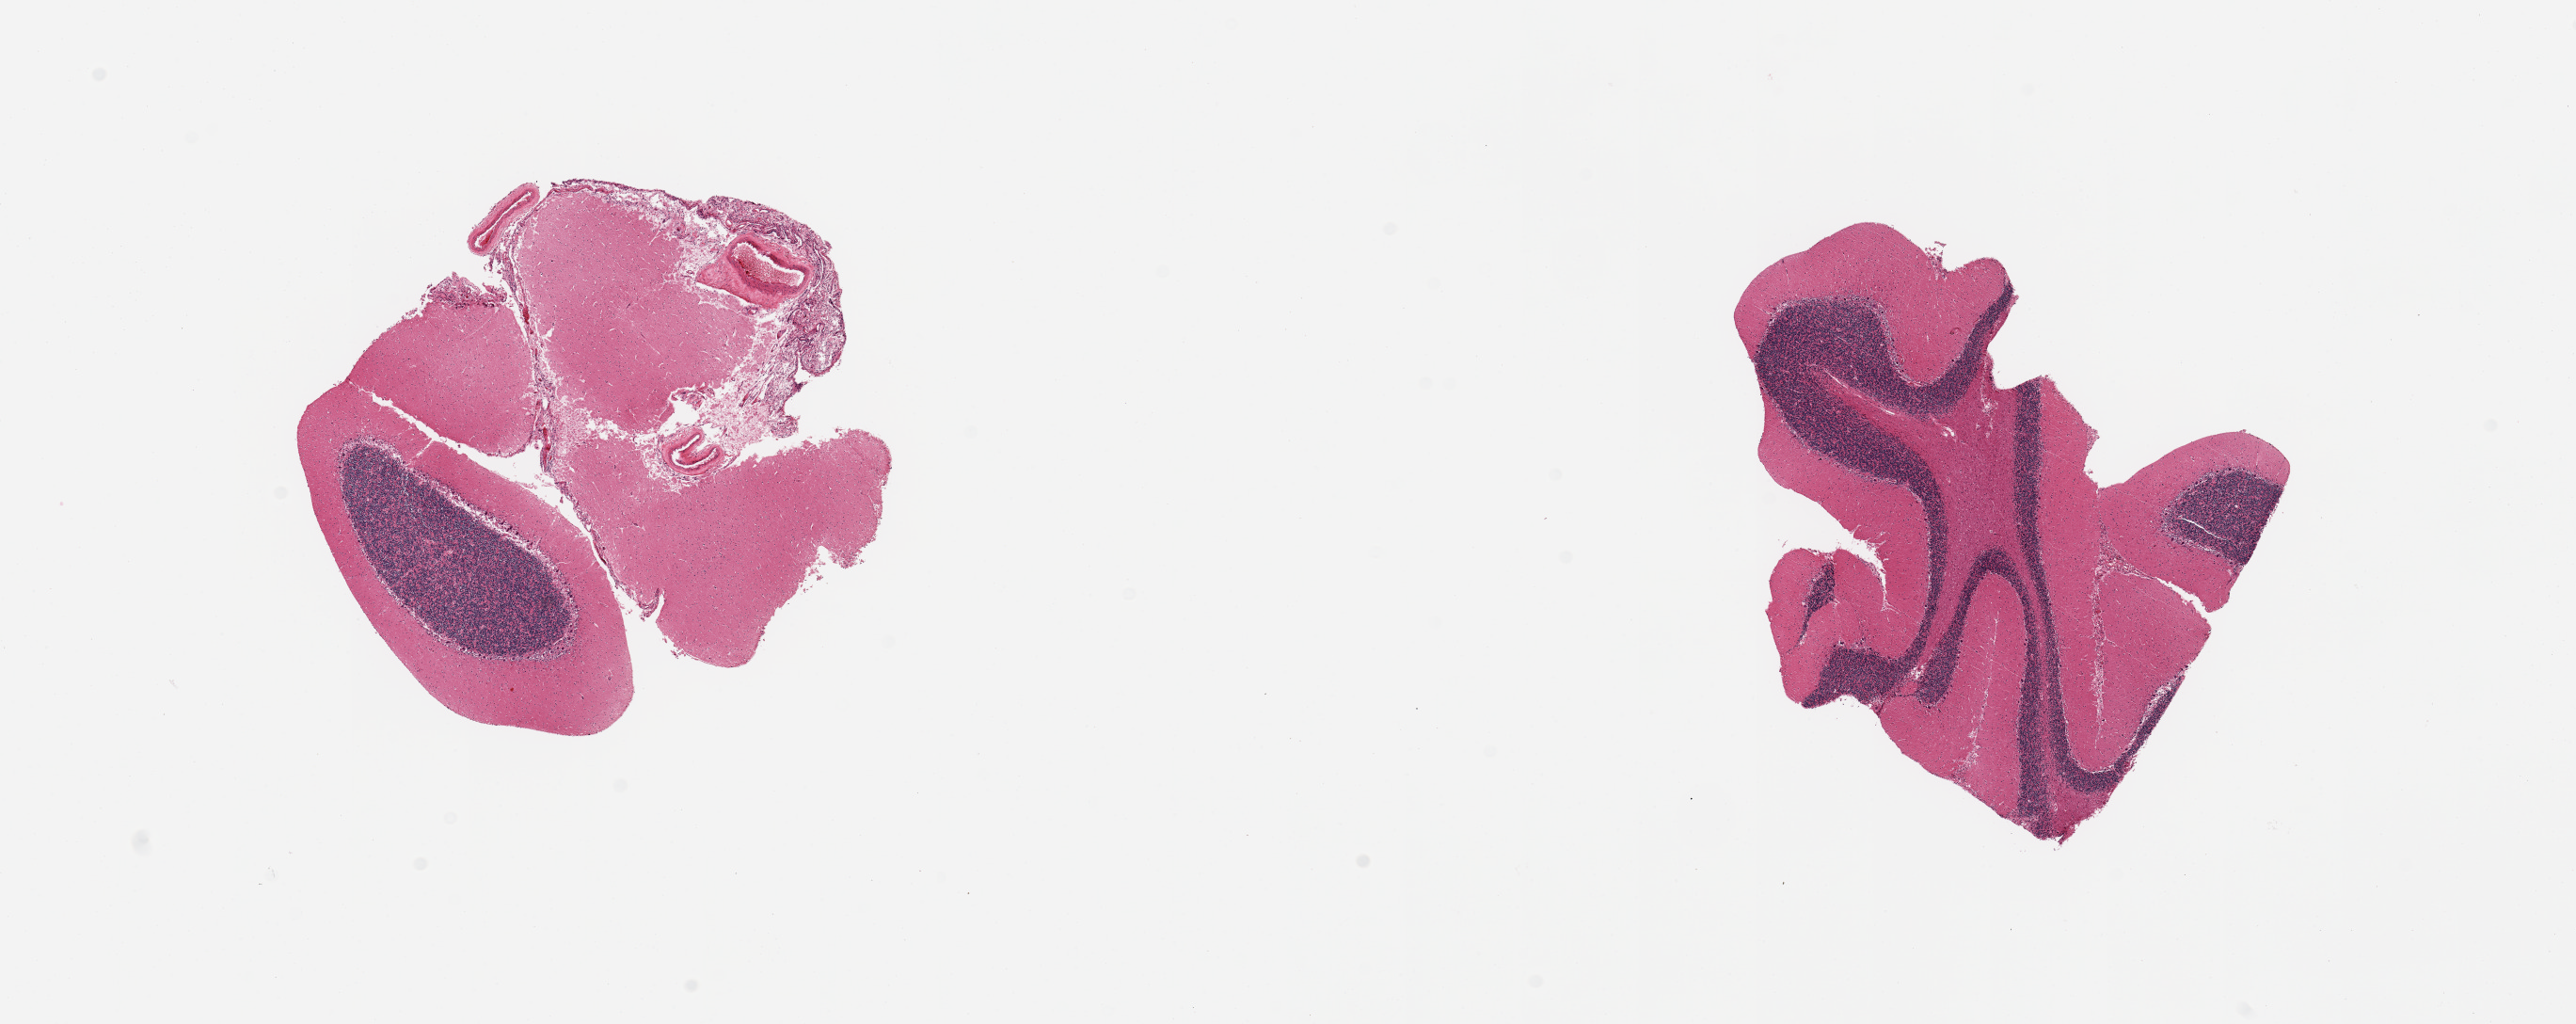
Digitized haematoxylin and eosin-stained section, brightfield — whole scanned area (about 21.7 x 8.6 mm) shown as a low-resolution overview. PAXgene-fixed, paraffin-embedded tissue. Target tissue: cerebellum. Donor tissue sample. Donor: male.
Review note (as recorded): 2 pieces; one piece with meninges.